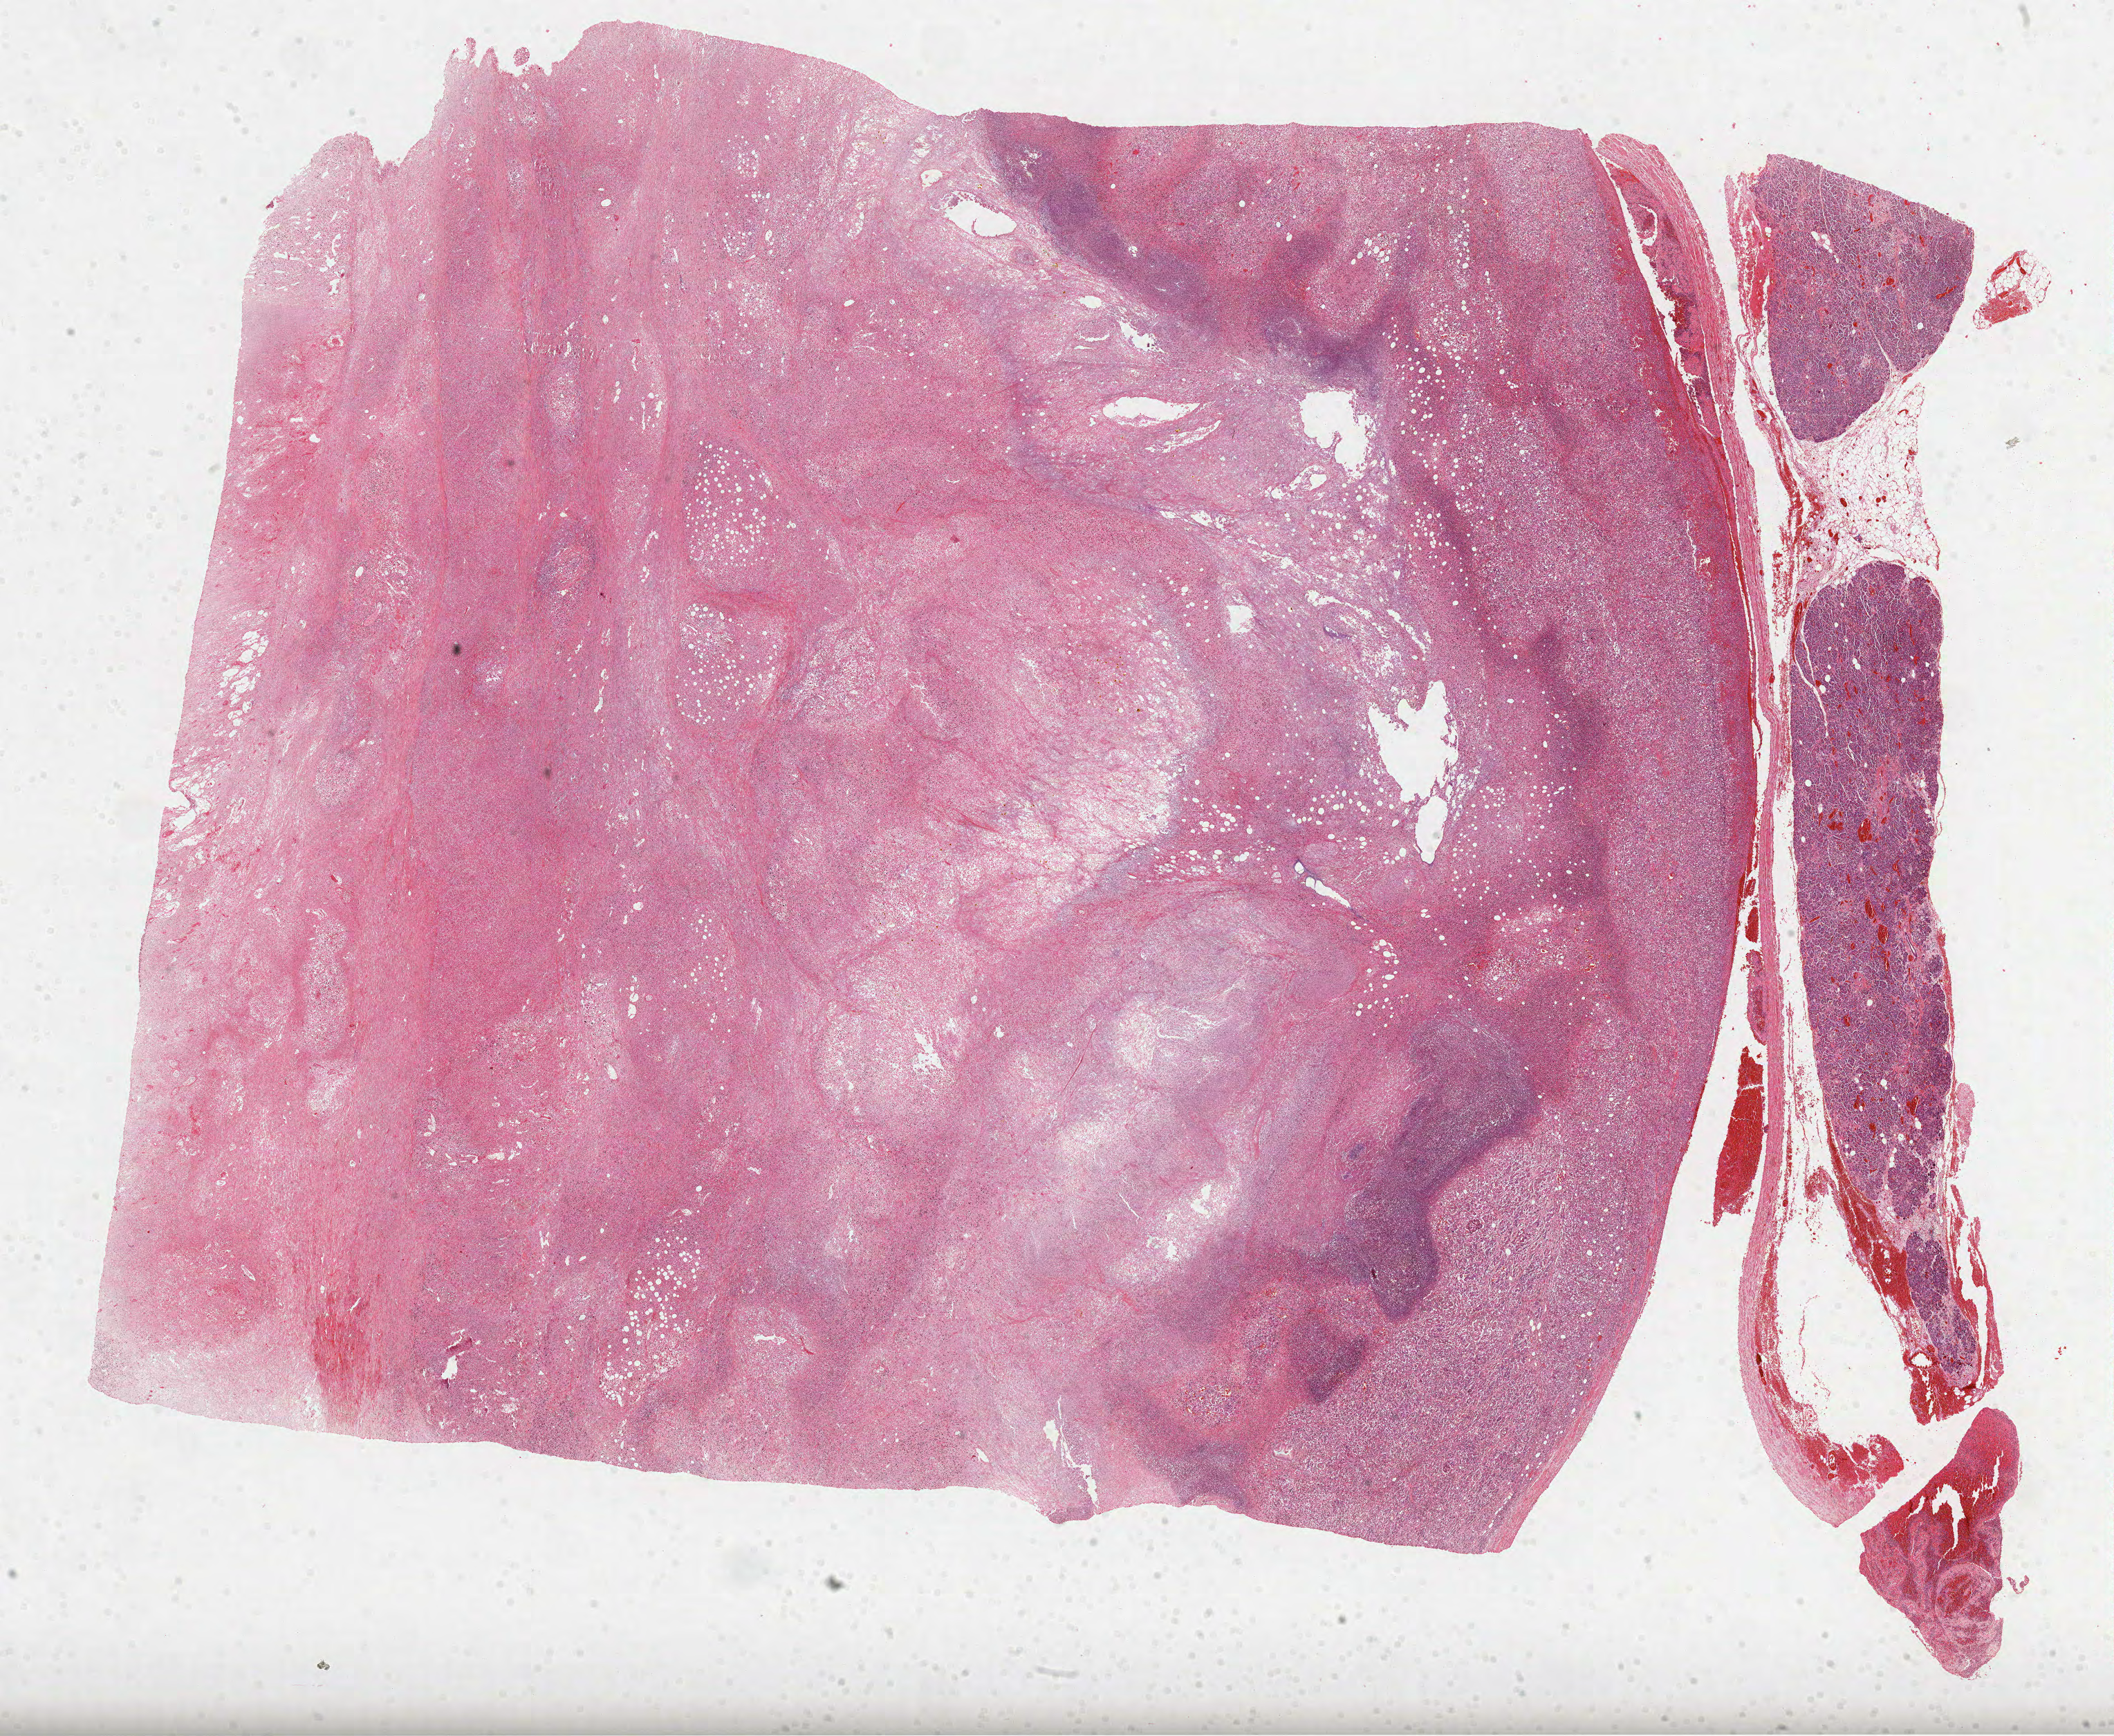
Whole-slide histology image, H&E — low-resolution overview of the scanned area, about 24.7 x 20.2 mm (from a 40x scan); formalin-fixed paraffin-embedded (FFPE) diagnostic section; kidney, primary tumour sample. Patient: male, age at initial diagnosis 75 years. Histologic grade: G4 (undifferentiated).
Lymph nodes positive (case pathology): 0 of 6 examined. AJCC pathologic stage: IV. Diagnosis: Clear cell adenocarcinoma, NOS.